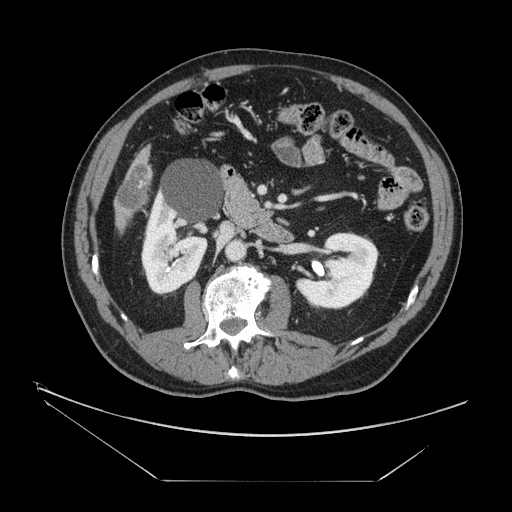
Contrast-enhanced abdominal CT, one axial slice. Reconstruction kernel STANDARD. 120 kVp. Intravenous contrast given. Soft-tissue window (W 400 / L 40 HU). 2.5 mm slice thickness. 512 × 512 image matrix, field of view 440 × 440 mm. Male patient, age 65 years. Case-level facts recorded for this patient, not image findings: diagnosis: colorectal cancer liver metastases, imaged before liver resection; multiple liver metastases: yes; largest metastasis: 4.2 cm; disease in both lobes: yes.
Annotated regions visible in this slice (outlined manually by an expert reader):
- liver: bounding box [x1, y1, x2, y2] px = [117, 152, 151, 225]
- liver metastasis: [119, 167, 151, 213]